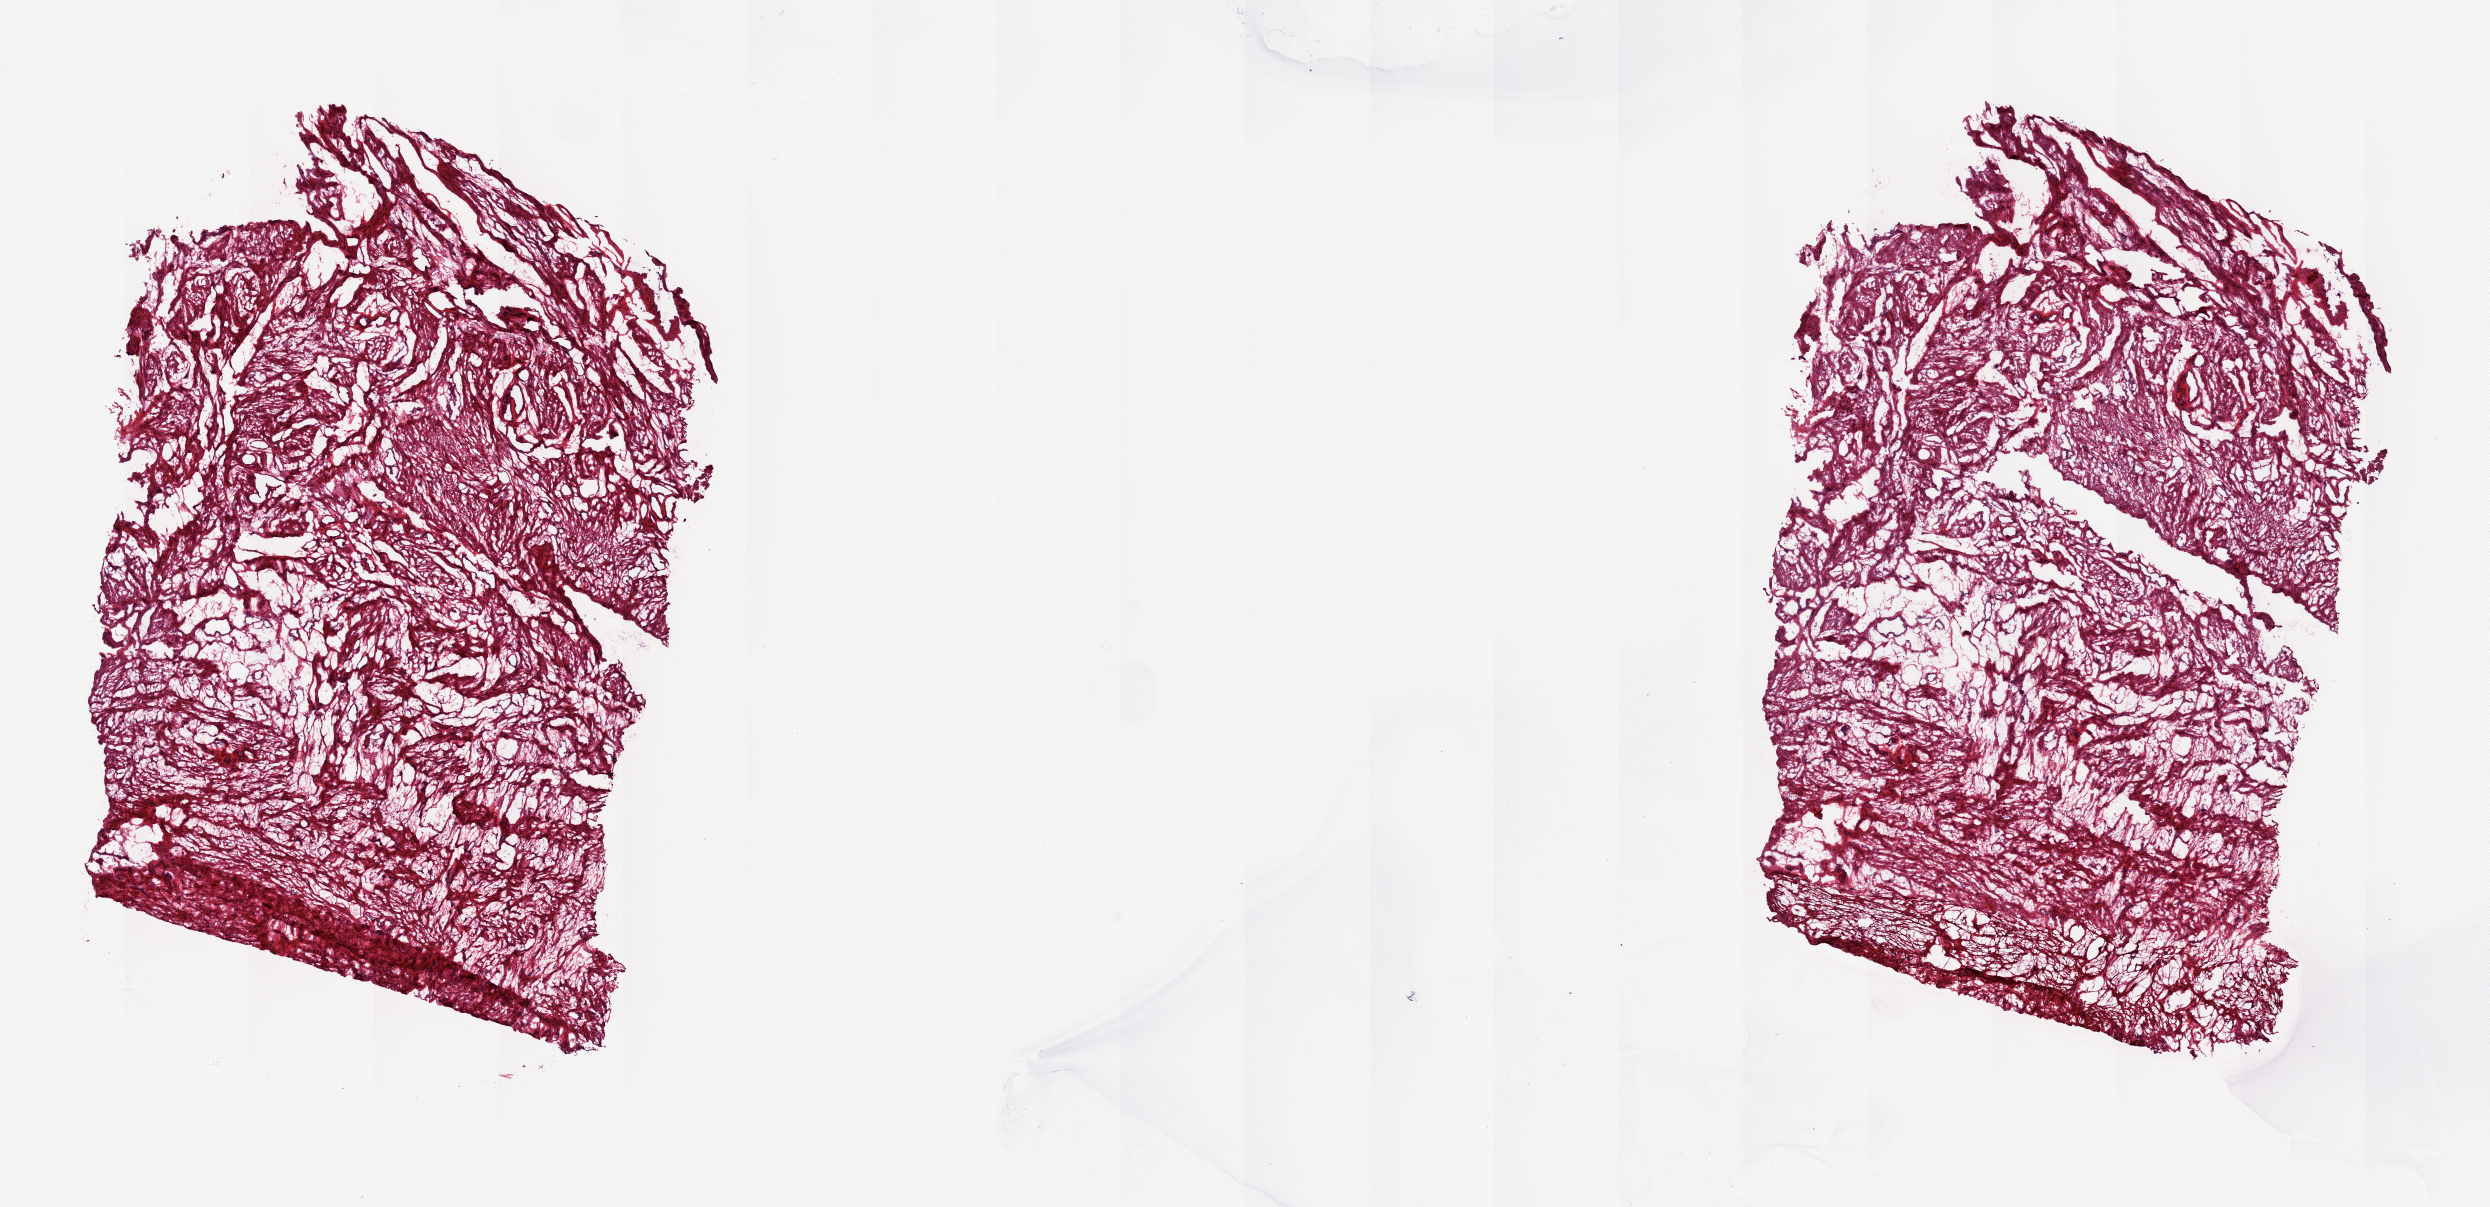
Whole-slide histology image, Hematoxylin and eosin (H&E) stained — low-resolution overview of the scanned area, about 19.7 x 9.5 mm (slide scanned at 20x); frozen section from the top of the tissue portion; sample: solid tissue normal (non-tumour tissue), uterus. Female patient; age at initial diagnosis 53 years. Composition of this section per pathologist review: tumour cells 0%, tumour nuclei 0%, normal cells 100%, stromal cells 0%, necrosis 0%. Infiltration values recorded for this section: lymphocyte infiltration 0%, monocyte infiltration 0%, neutrophil infiltration 0%.
This section: solid tissue normal sample (biorepository sample class). Patient diagnosis: Endometrioid adenocarcinoma, NOS.